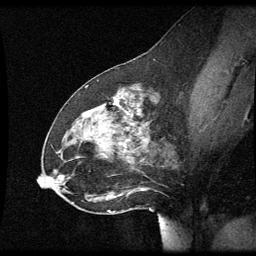
Breast MRI (dynamic contrast-enhanced), one sagittal slice. Position 29 of 60 along the scan axis. Dynamic contrast-enhanced series, image 2 of 3 at this slice position (ordered by acquisition). 1.5 T. TE 4.2 ms, TR 8.9 ms. 2 mm slice thickness. 256 × 256 image matrix. Patient: female, 49 years. From the clinical record (not read from this slice): setting: breast cancer imaged before/during neoadjuvant chemotherapy; receptor status: HR-positive, HER2-negative.
Outlined on this slice (semi-automatically segmented with operator editing):
- analysis volume of interest (the breast-tissue region the enhancement analysis was run in; not a lesion): bounding box (x1, y1, x2, y2) in pixels: (46, 92, 175, 205)
- tumour enhancement mask (voxels above the 70 % enhancement threshold inside the analysis volume of interest): (115, 98, 141, 117)